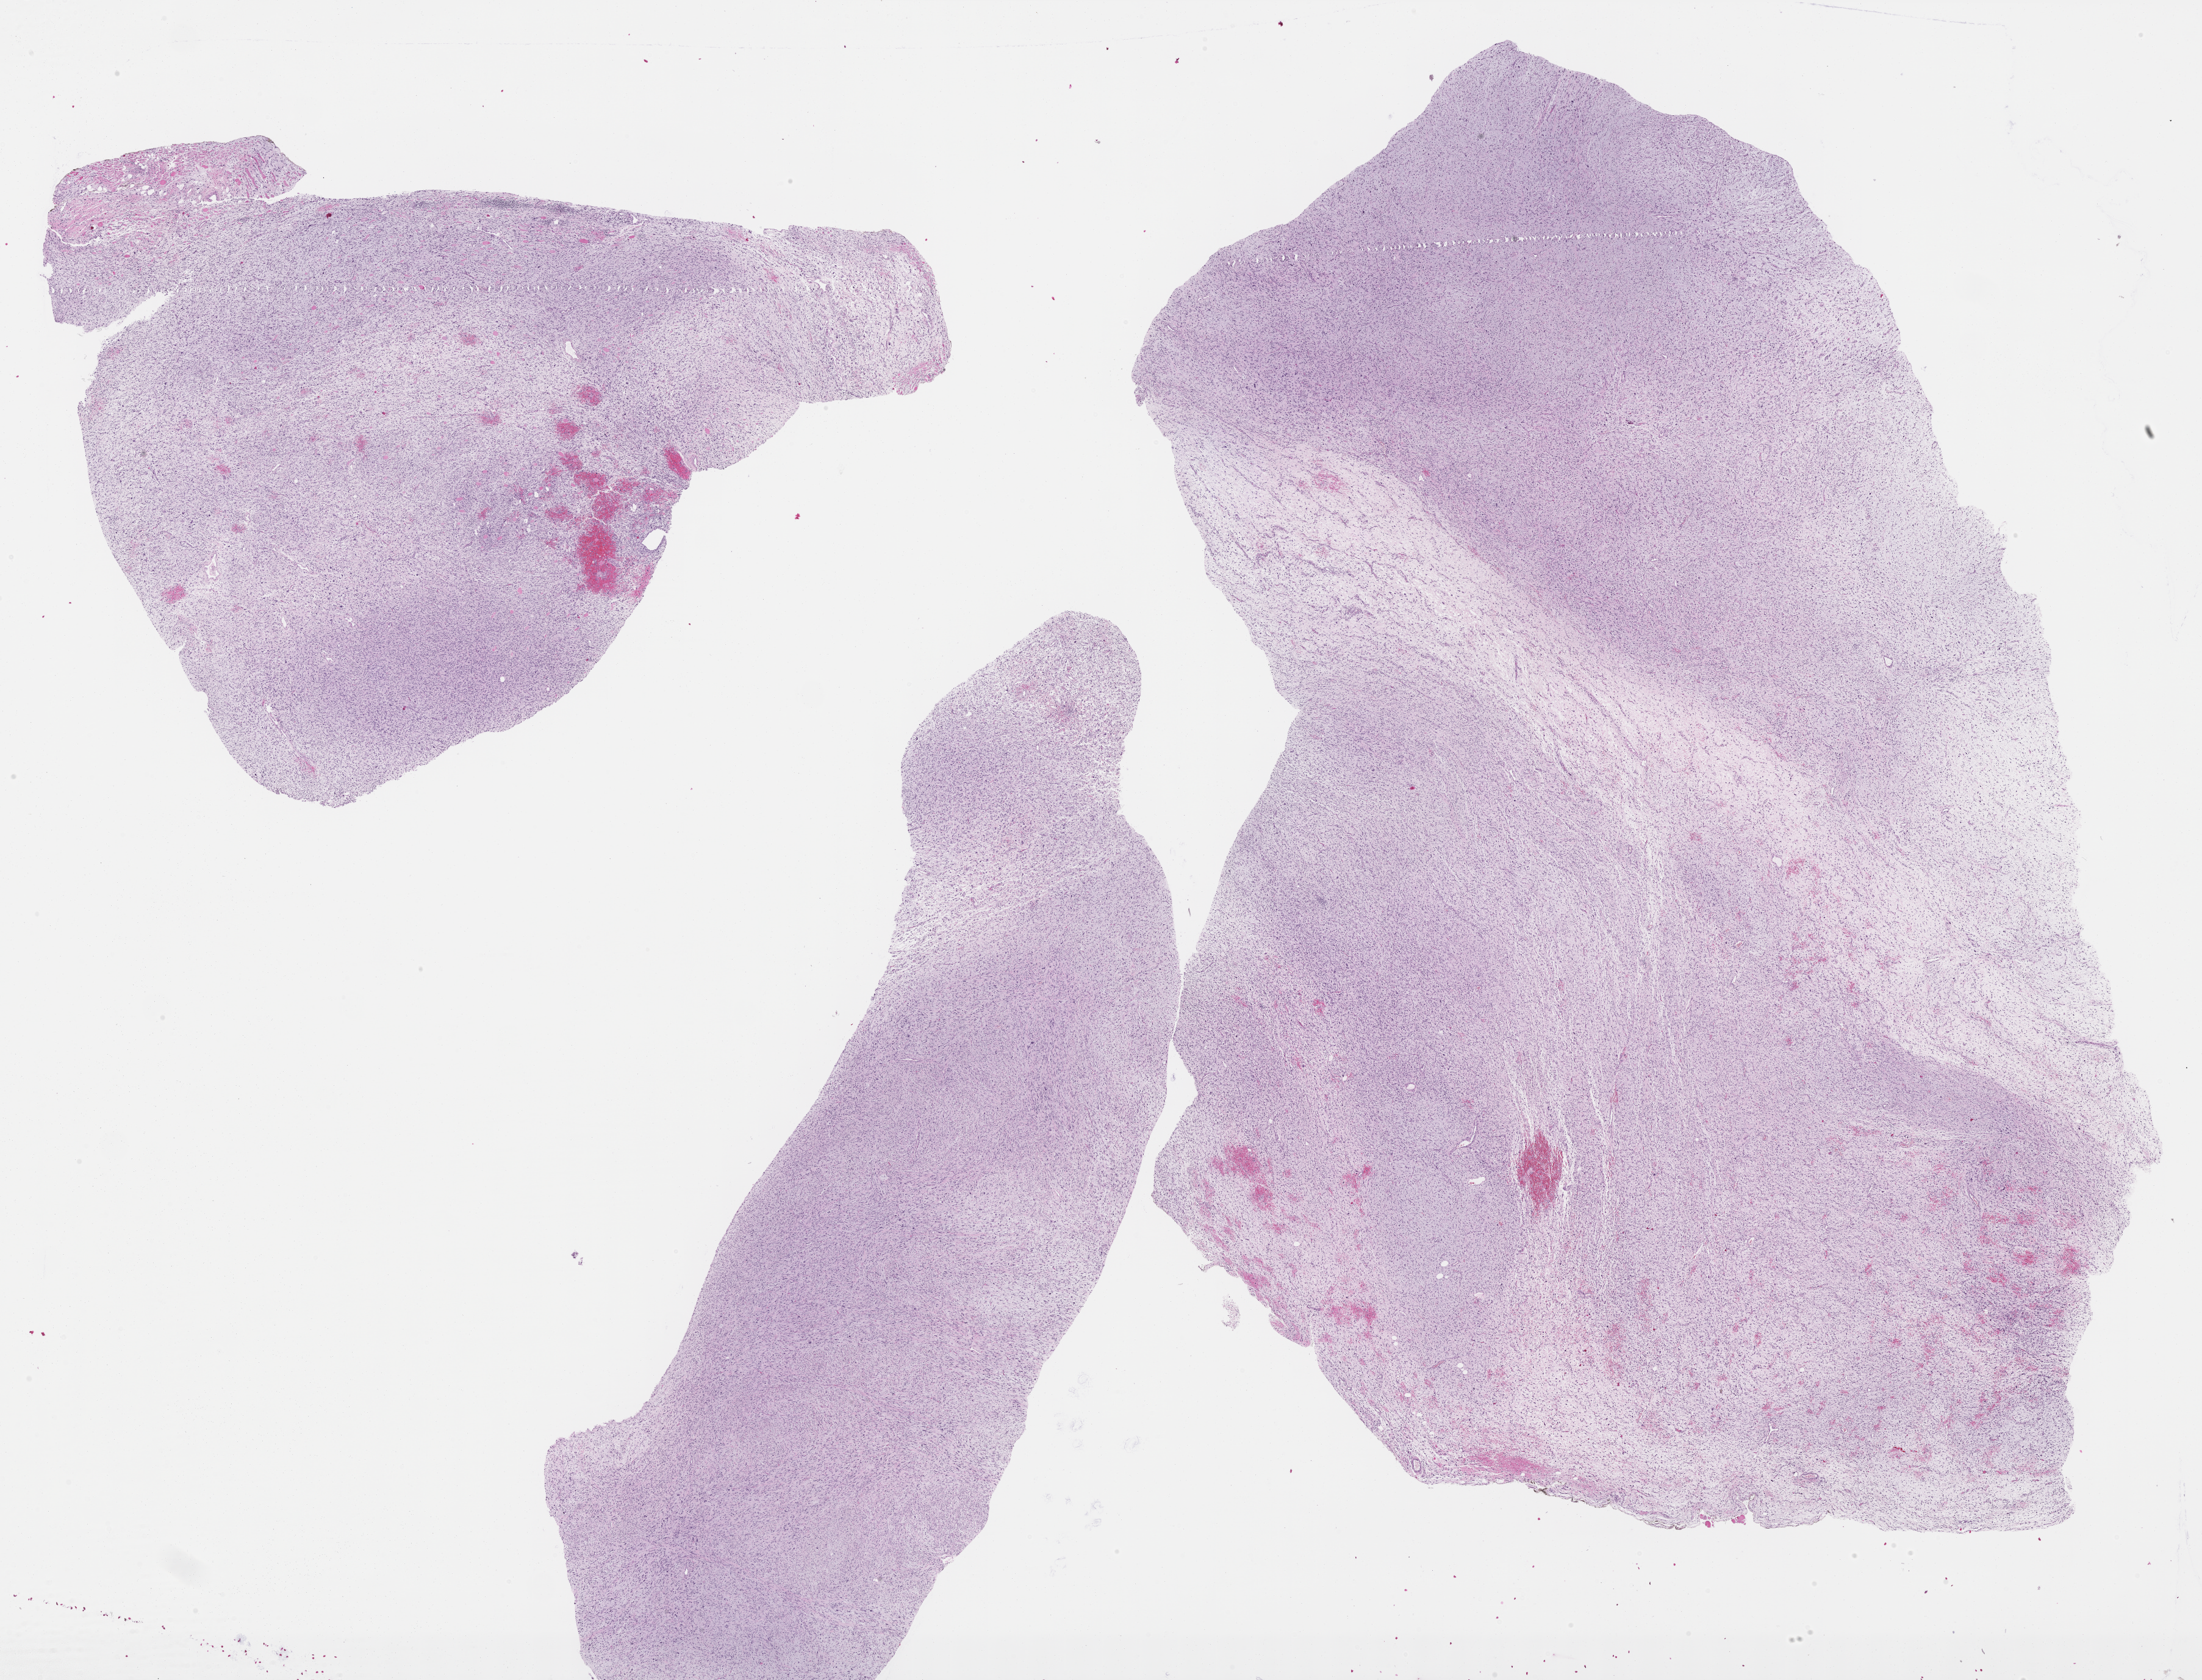
Digitized H&E tissue section (whole slide) — shown as a low-resolution overview of the whole scanned area (about 29.0 x 22.1 mm, from a 40x scan), formalin-fixed paraffin-embedded (FFPE) diagnostic section, primary tumour sample from the retroperitoneum and peritoneum. Female patient; age at initial diagnosis 79 years.
- diagnosis: Fibromyxosarcoma